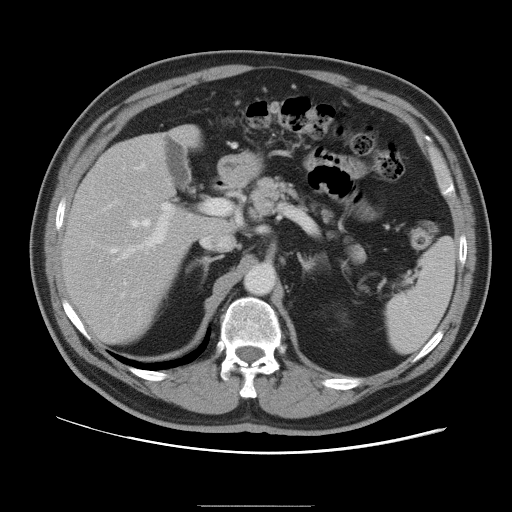
Contrast-enhanced abdominal CT, one axial slice. Slice 59 of 105 in the series (ordered by position). 120 kVp. Intravenous contrast given. Soft-tissue window (W 400 / L 40 HU). 5 mm slice thickness. 512 × 512 image matrix, field of view 399 × 399 mm. Male patient, age 64 years. From the clinical record (not read from this slice): diagnosis: colorectal cancer liver metastases, imaged before liver resection; multiple liver metastases: yes; largest metastasis: 3 cm; disease in both lobes: yes.
Outlined on this slice (manually delineated by an expert):
- hepatic veins: bounding box <111,164,150,284> (left, top, right, bottom; pixels)
- liver: <63,128,228,343>
- planned liver remnant (the part of the liver to remain after resection): <64,136,229,343>
- portal vein (with intrahepatic branches): <117,203,174,318>